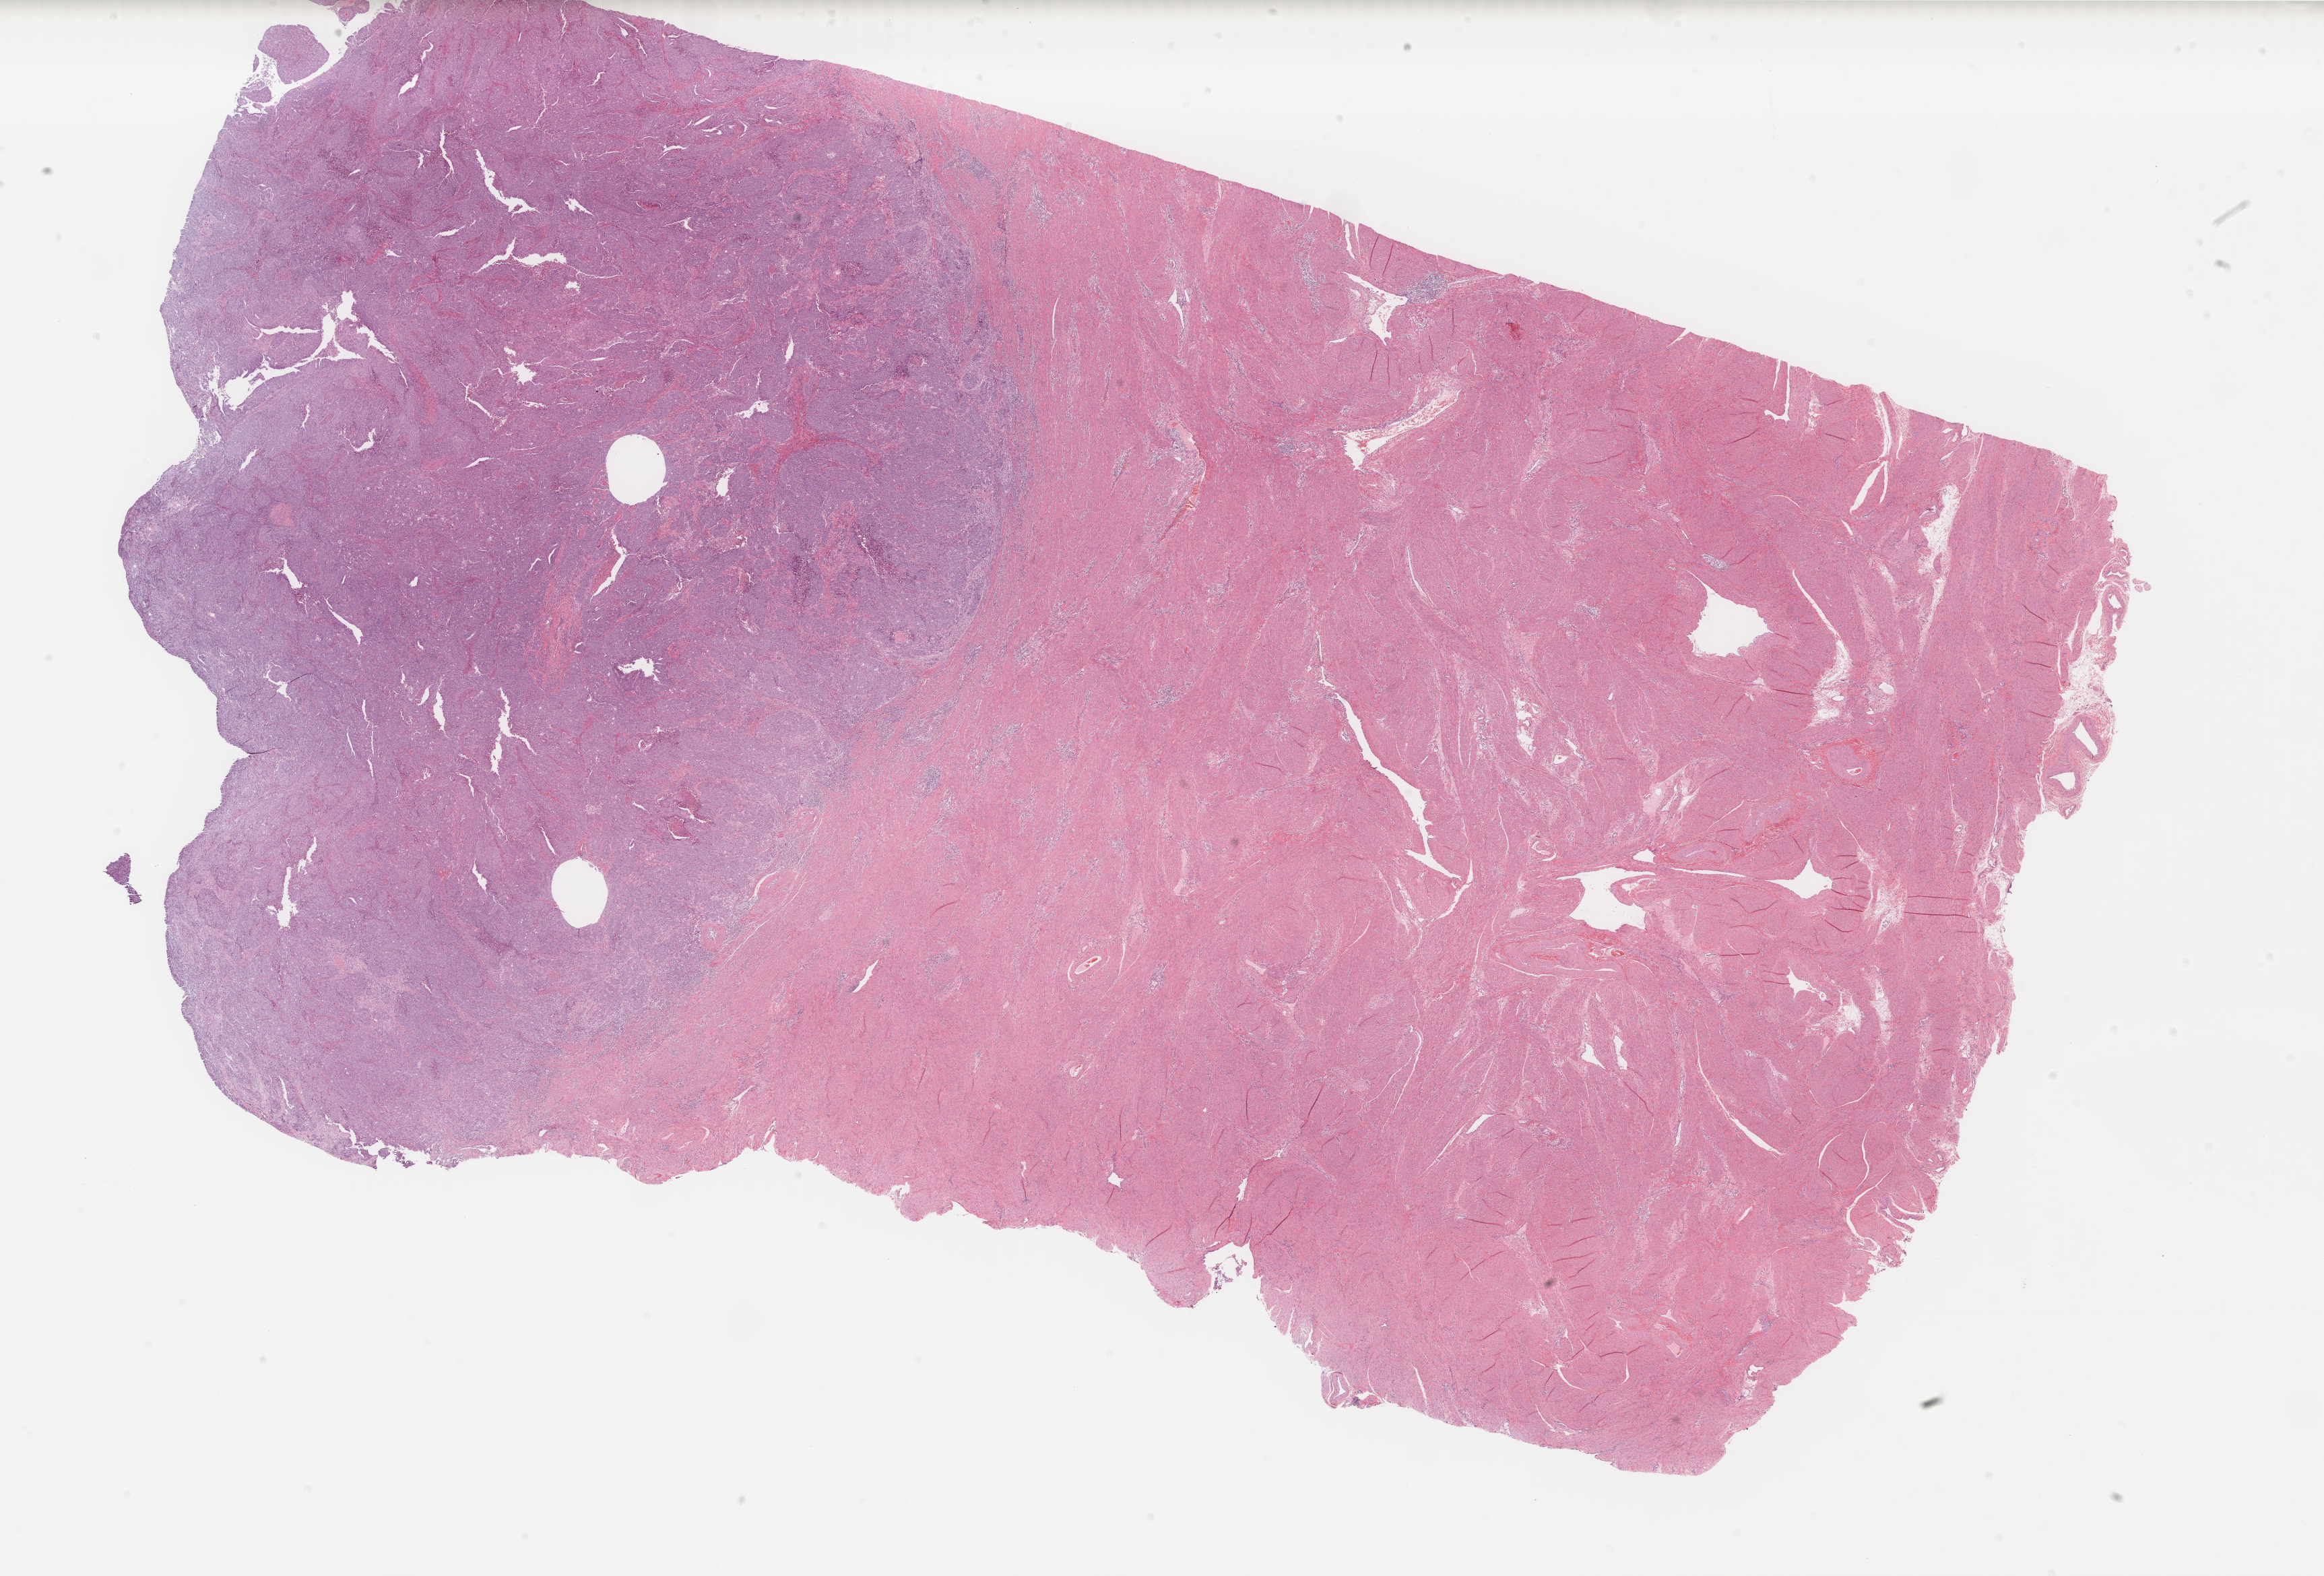
H&E-stained whole-slide image, a low-resolution overview of the entire scanned area, about 27.4 x 18.6 mm; FFPE section; sample: primary tumour, uterus. Female patient; age at initial diagnosis 40 years. Histologic grade: G3 (poorly differentiated).
- diagnosis: Endometrioid adenocarcinoma, NOS (endometrium)
- FIGO stage: IB